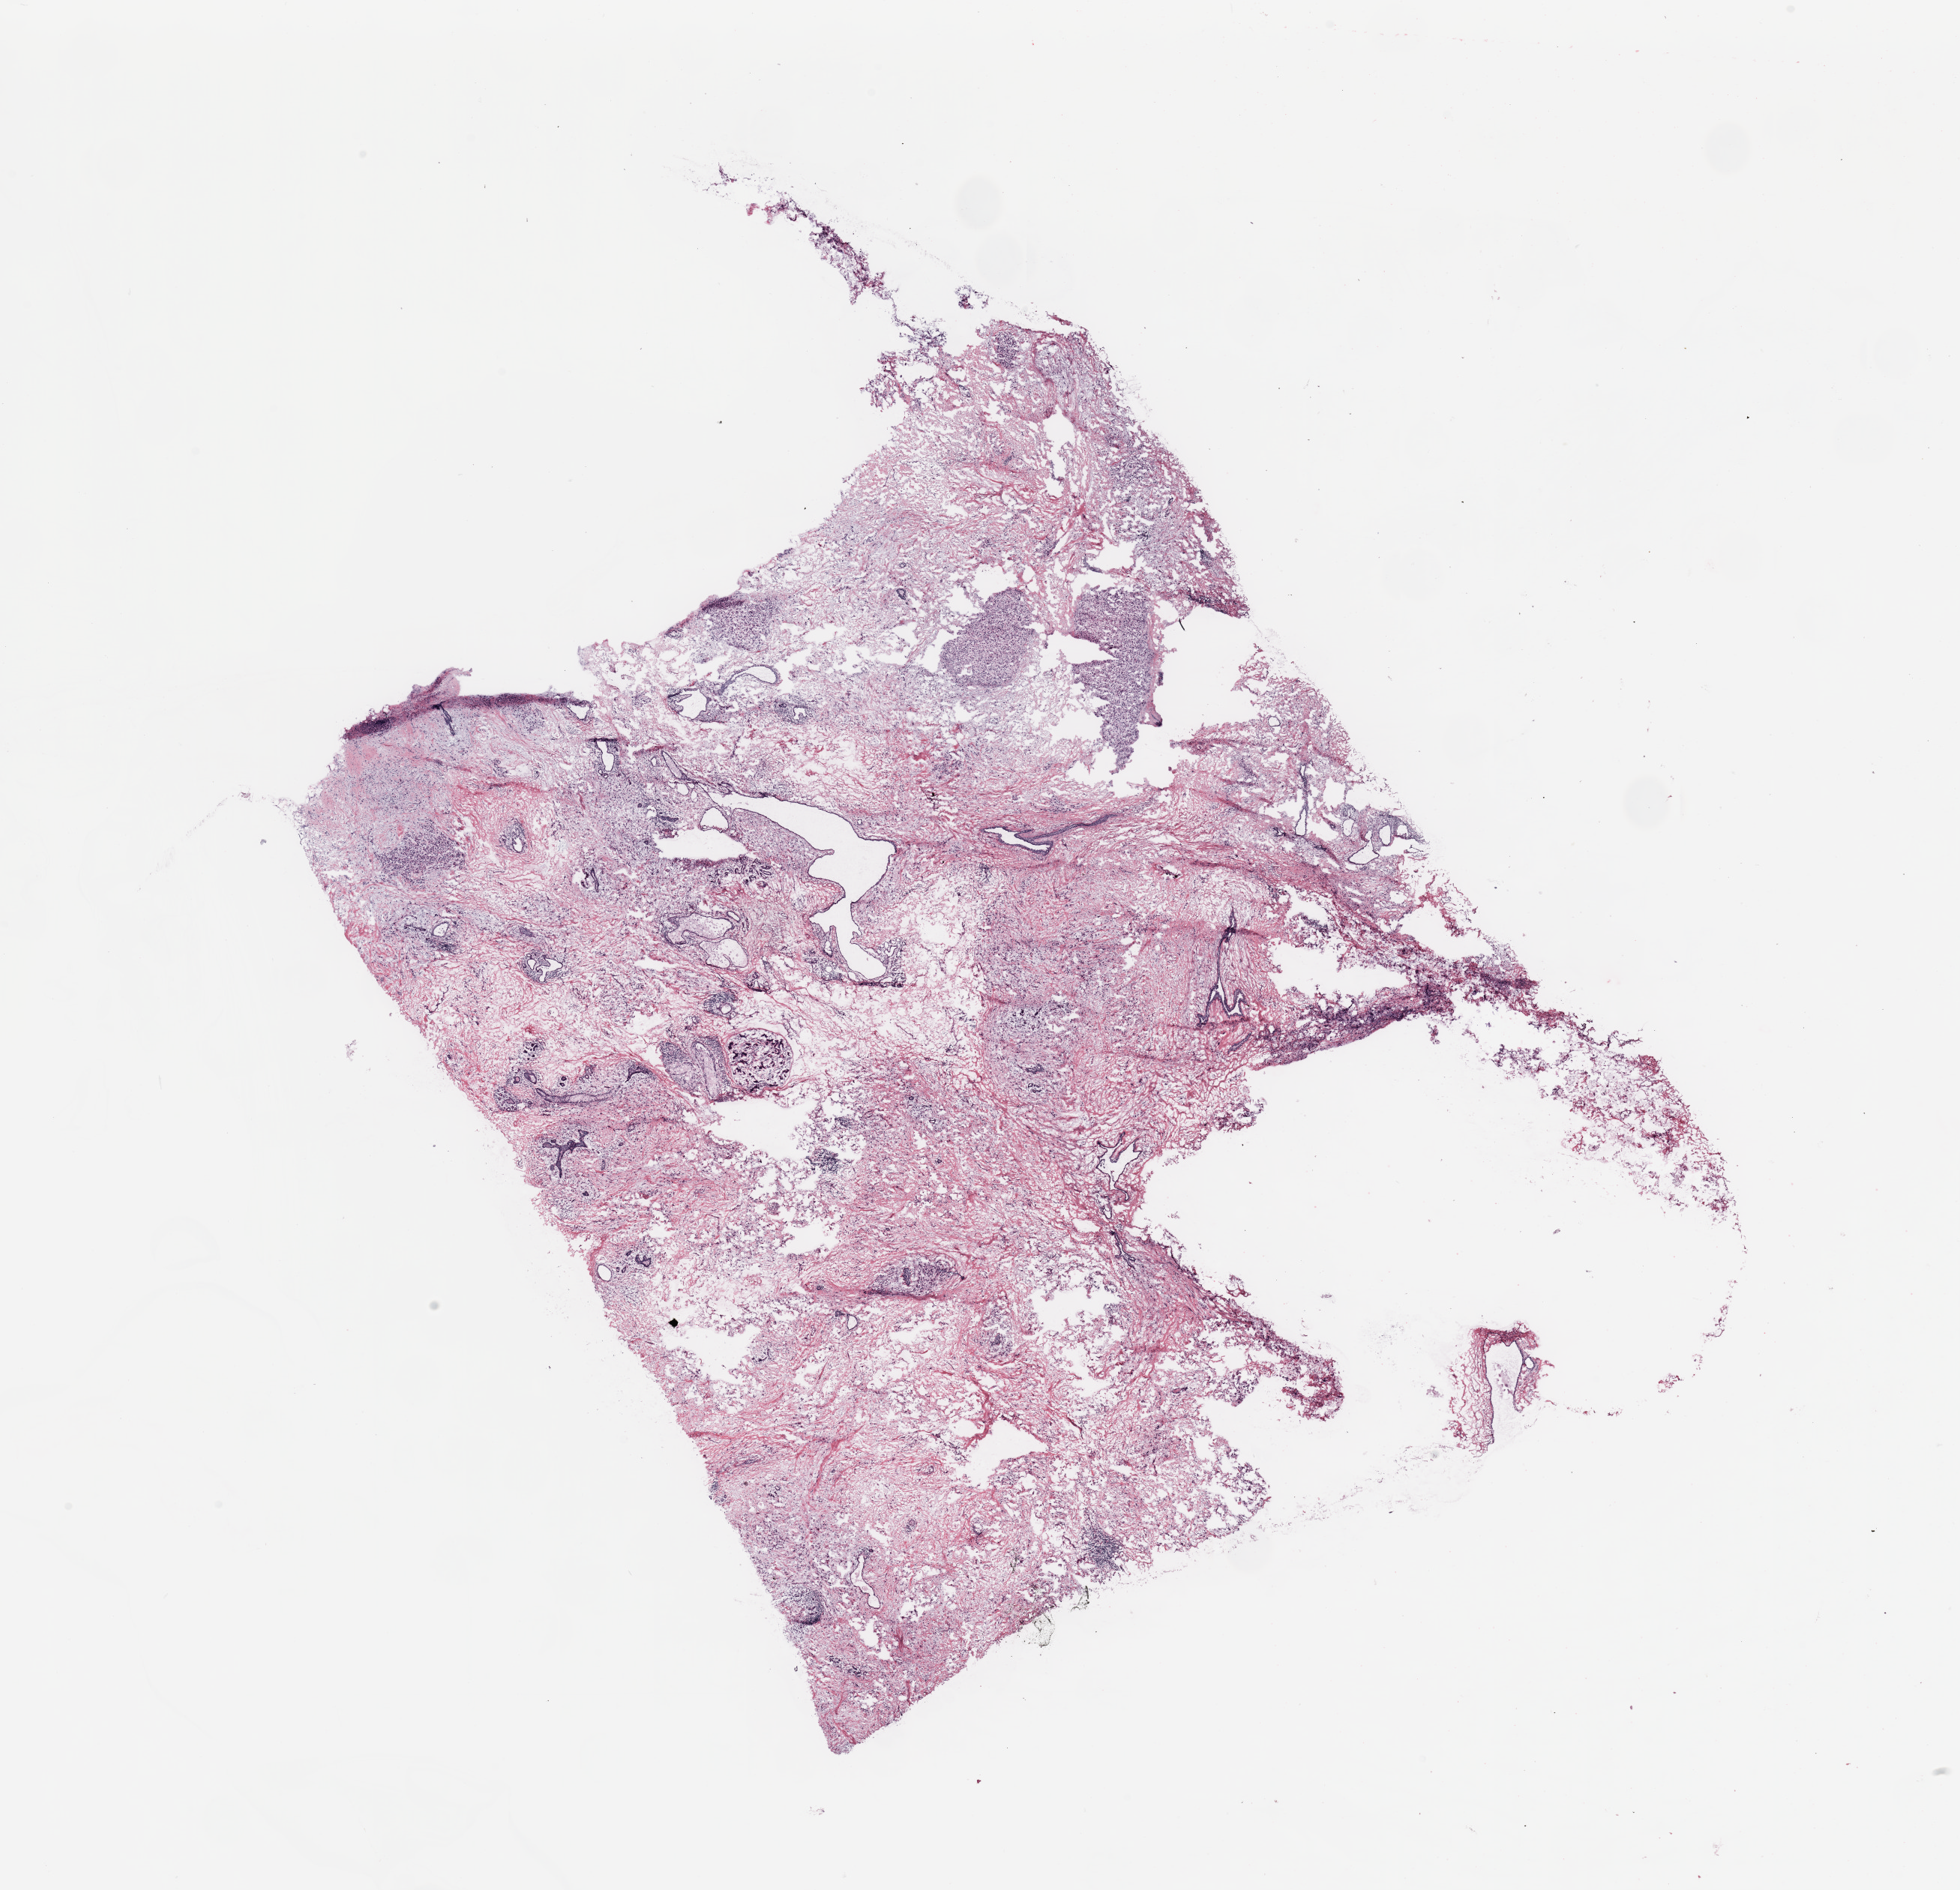
Digitized H&E-stained tissue section (whole slide), low-resolution overview of the scanned area, about 20.7 x 19.9 mm; breast, tissue type not recorded.
* patient diagnosis (cohort enrolment): breast cancer (breast)